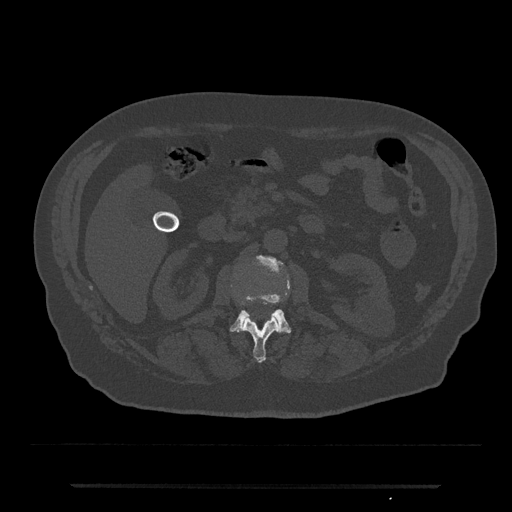
CT including the spine, one axial slice. Position 504 of 797 along the scan axis. Reconstruction kernel Br40s/3. 120 kVp. Bone window (W 1800 / L 400 HU). 0.5 mm slice thickness. 512 × 512 image matrix. Male patient, age 80 years. From the clinical record (not read from this slice): primary cancer: prostate; vertebrae with lytic lesions (as recorded): L1, T11.
Structures marked on this image (semi-automatically segmented with operator editing):
- L1 vertebra: bounding box (x1, y1, x2, y2) in pixels: (243, 317, 280, 363)
- L2 vertebra: (230, 256, 291, 334)